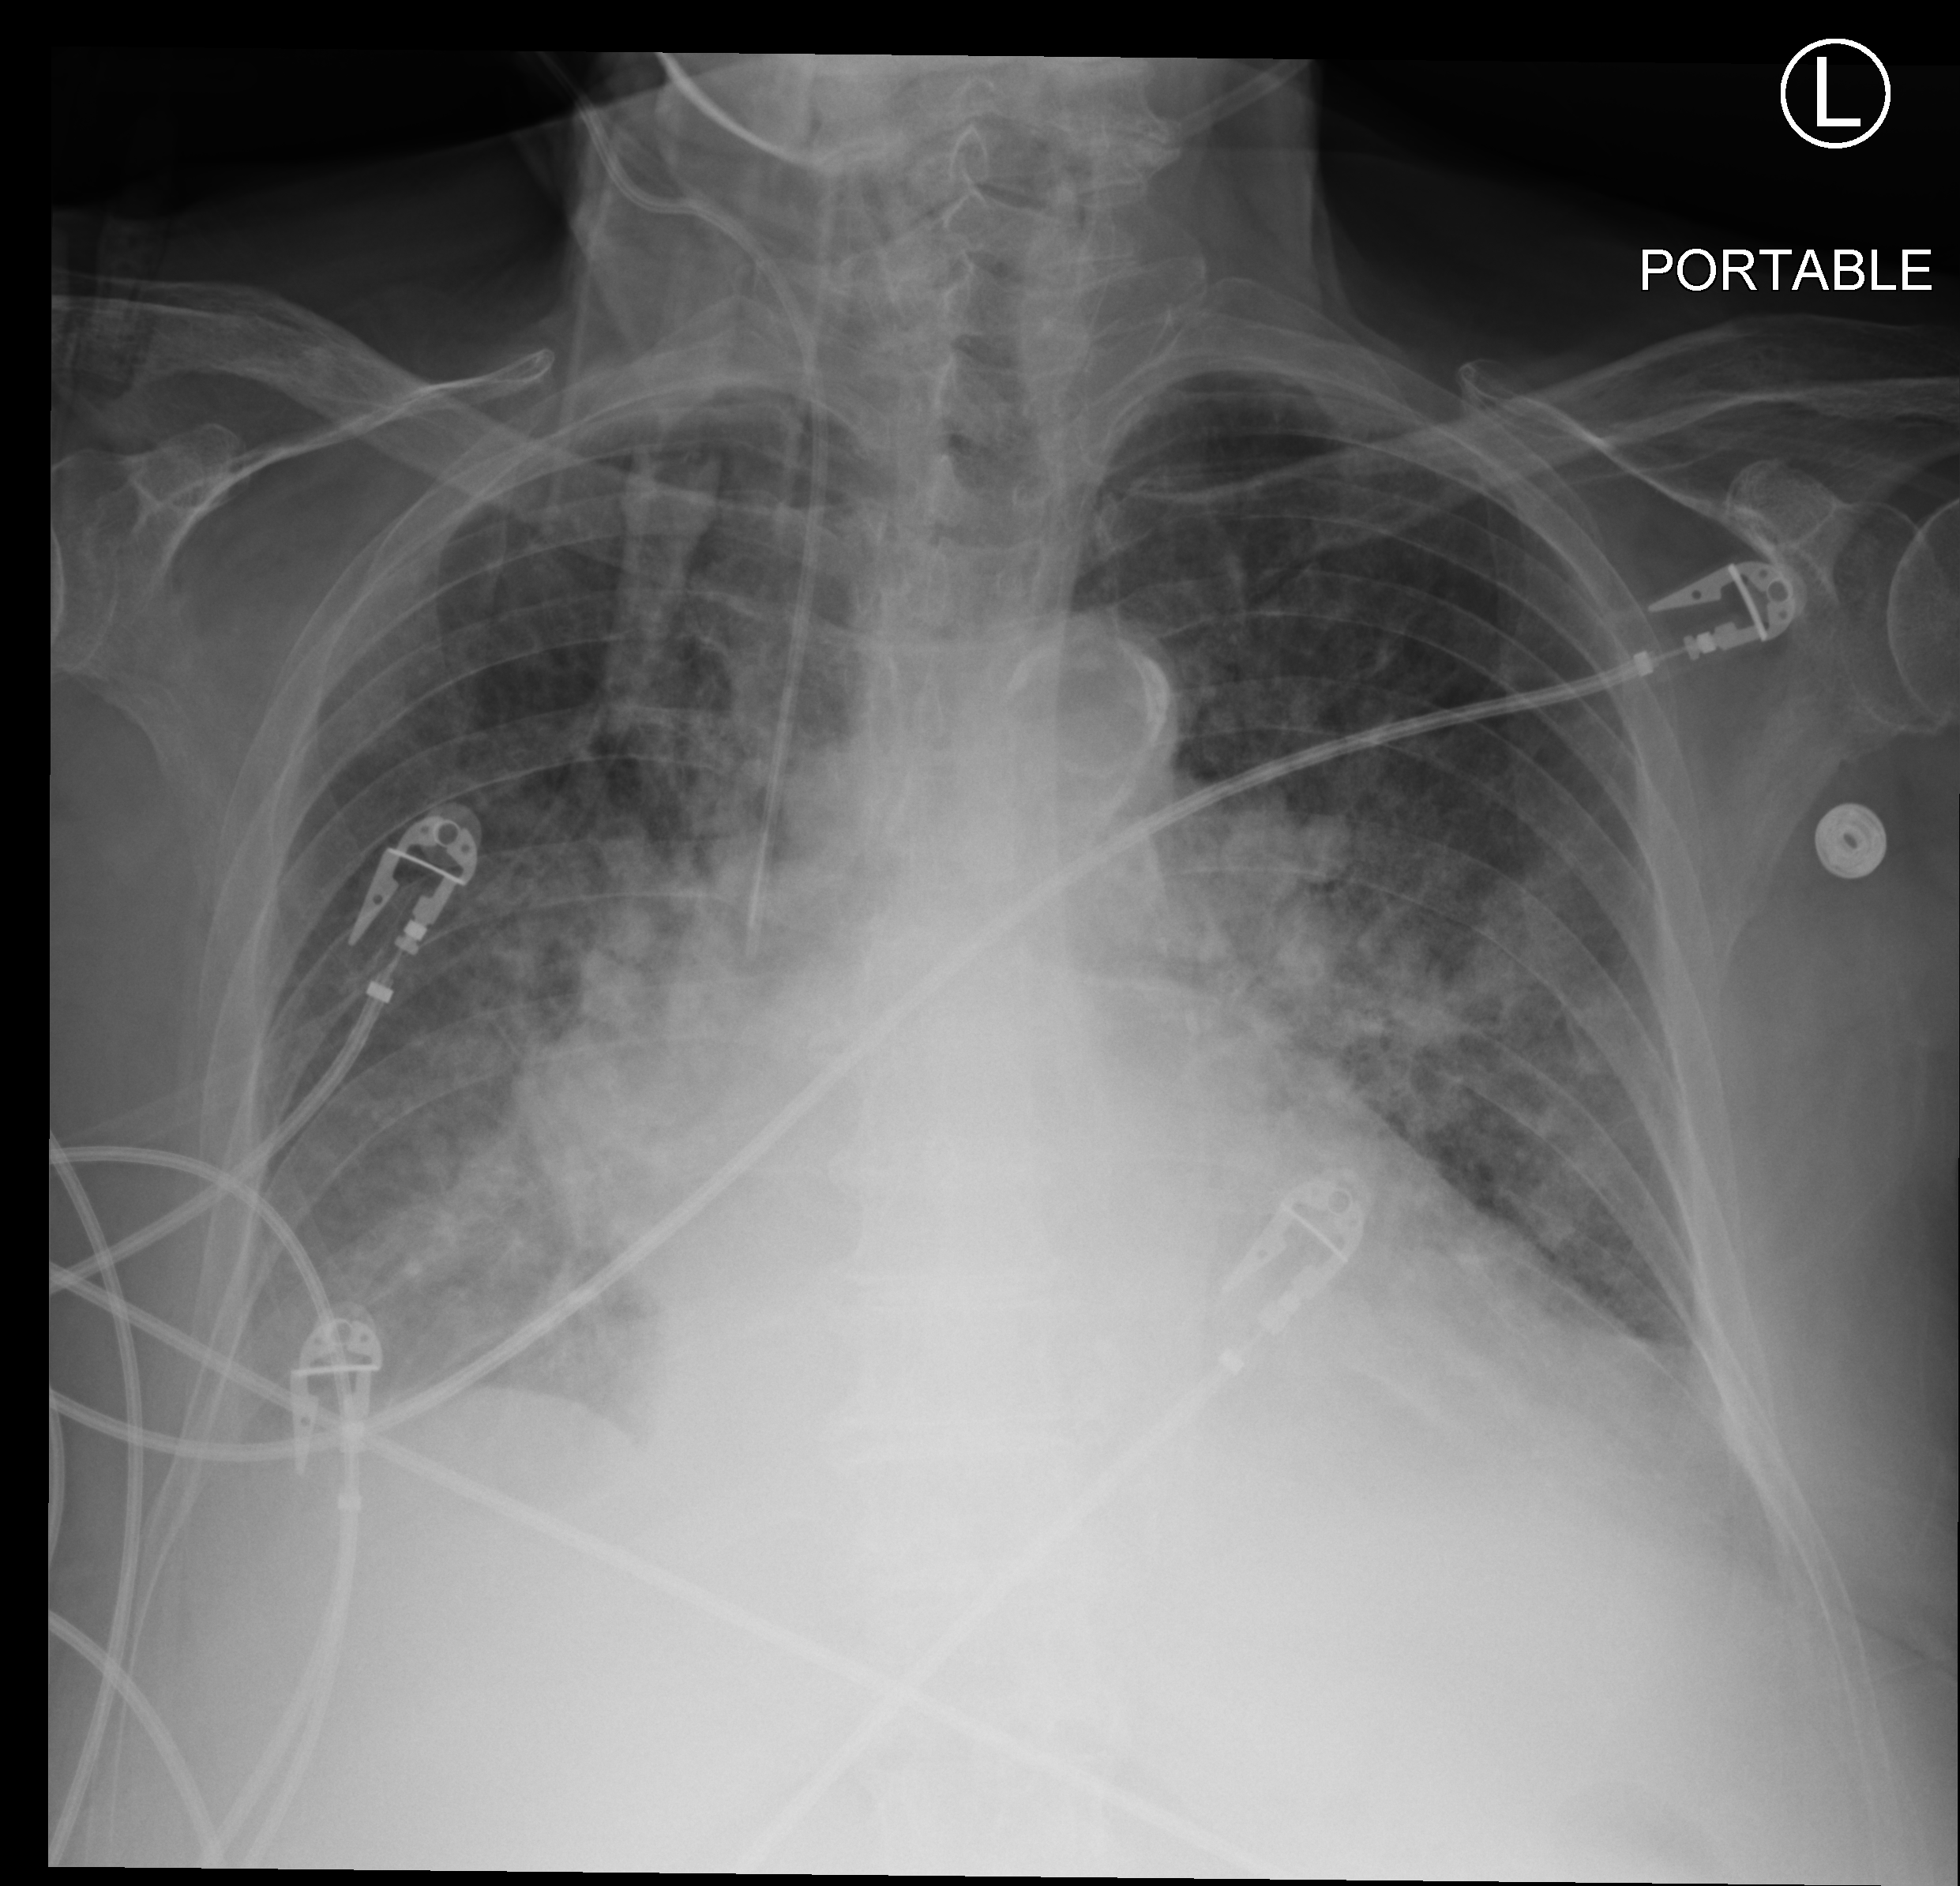
Portable chest radiograph. Patient hospitalised with COVID-19; female, aged 75–90 years.
Admission-level facts for this patient (not findings on this image; timing relative to this image not recorded): COPD (admission record): yes.